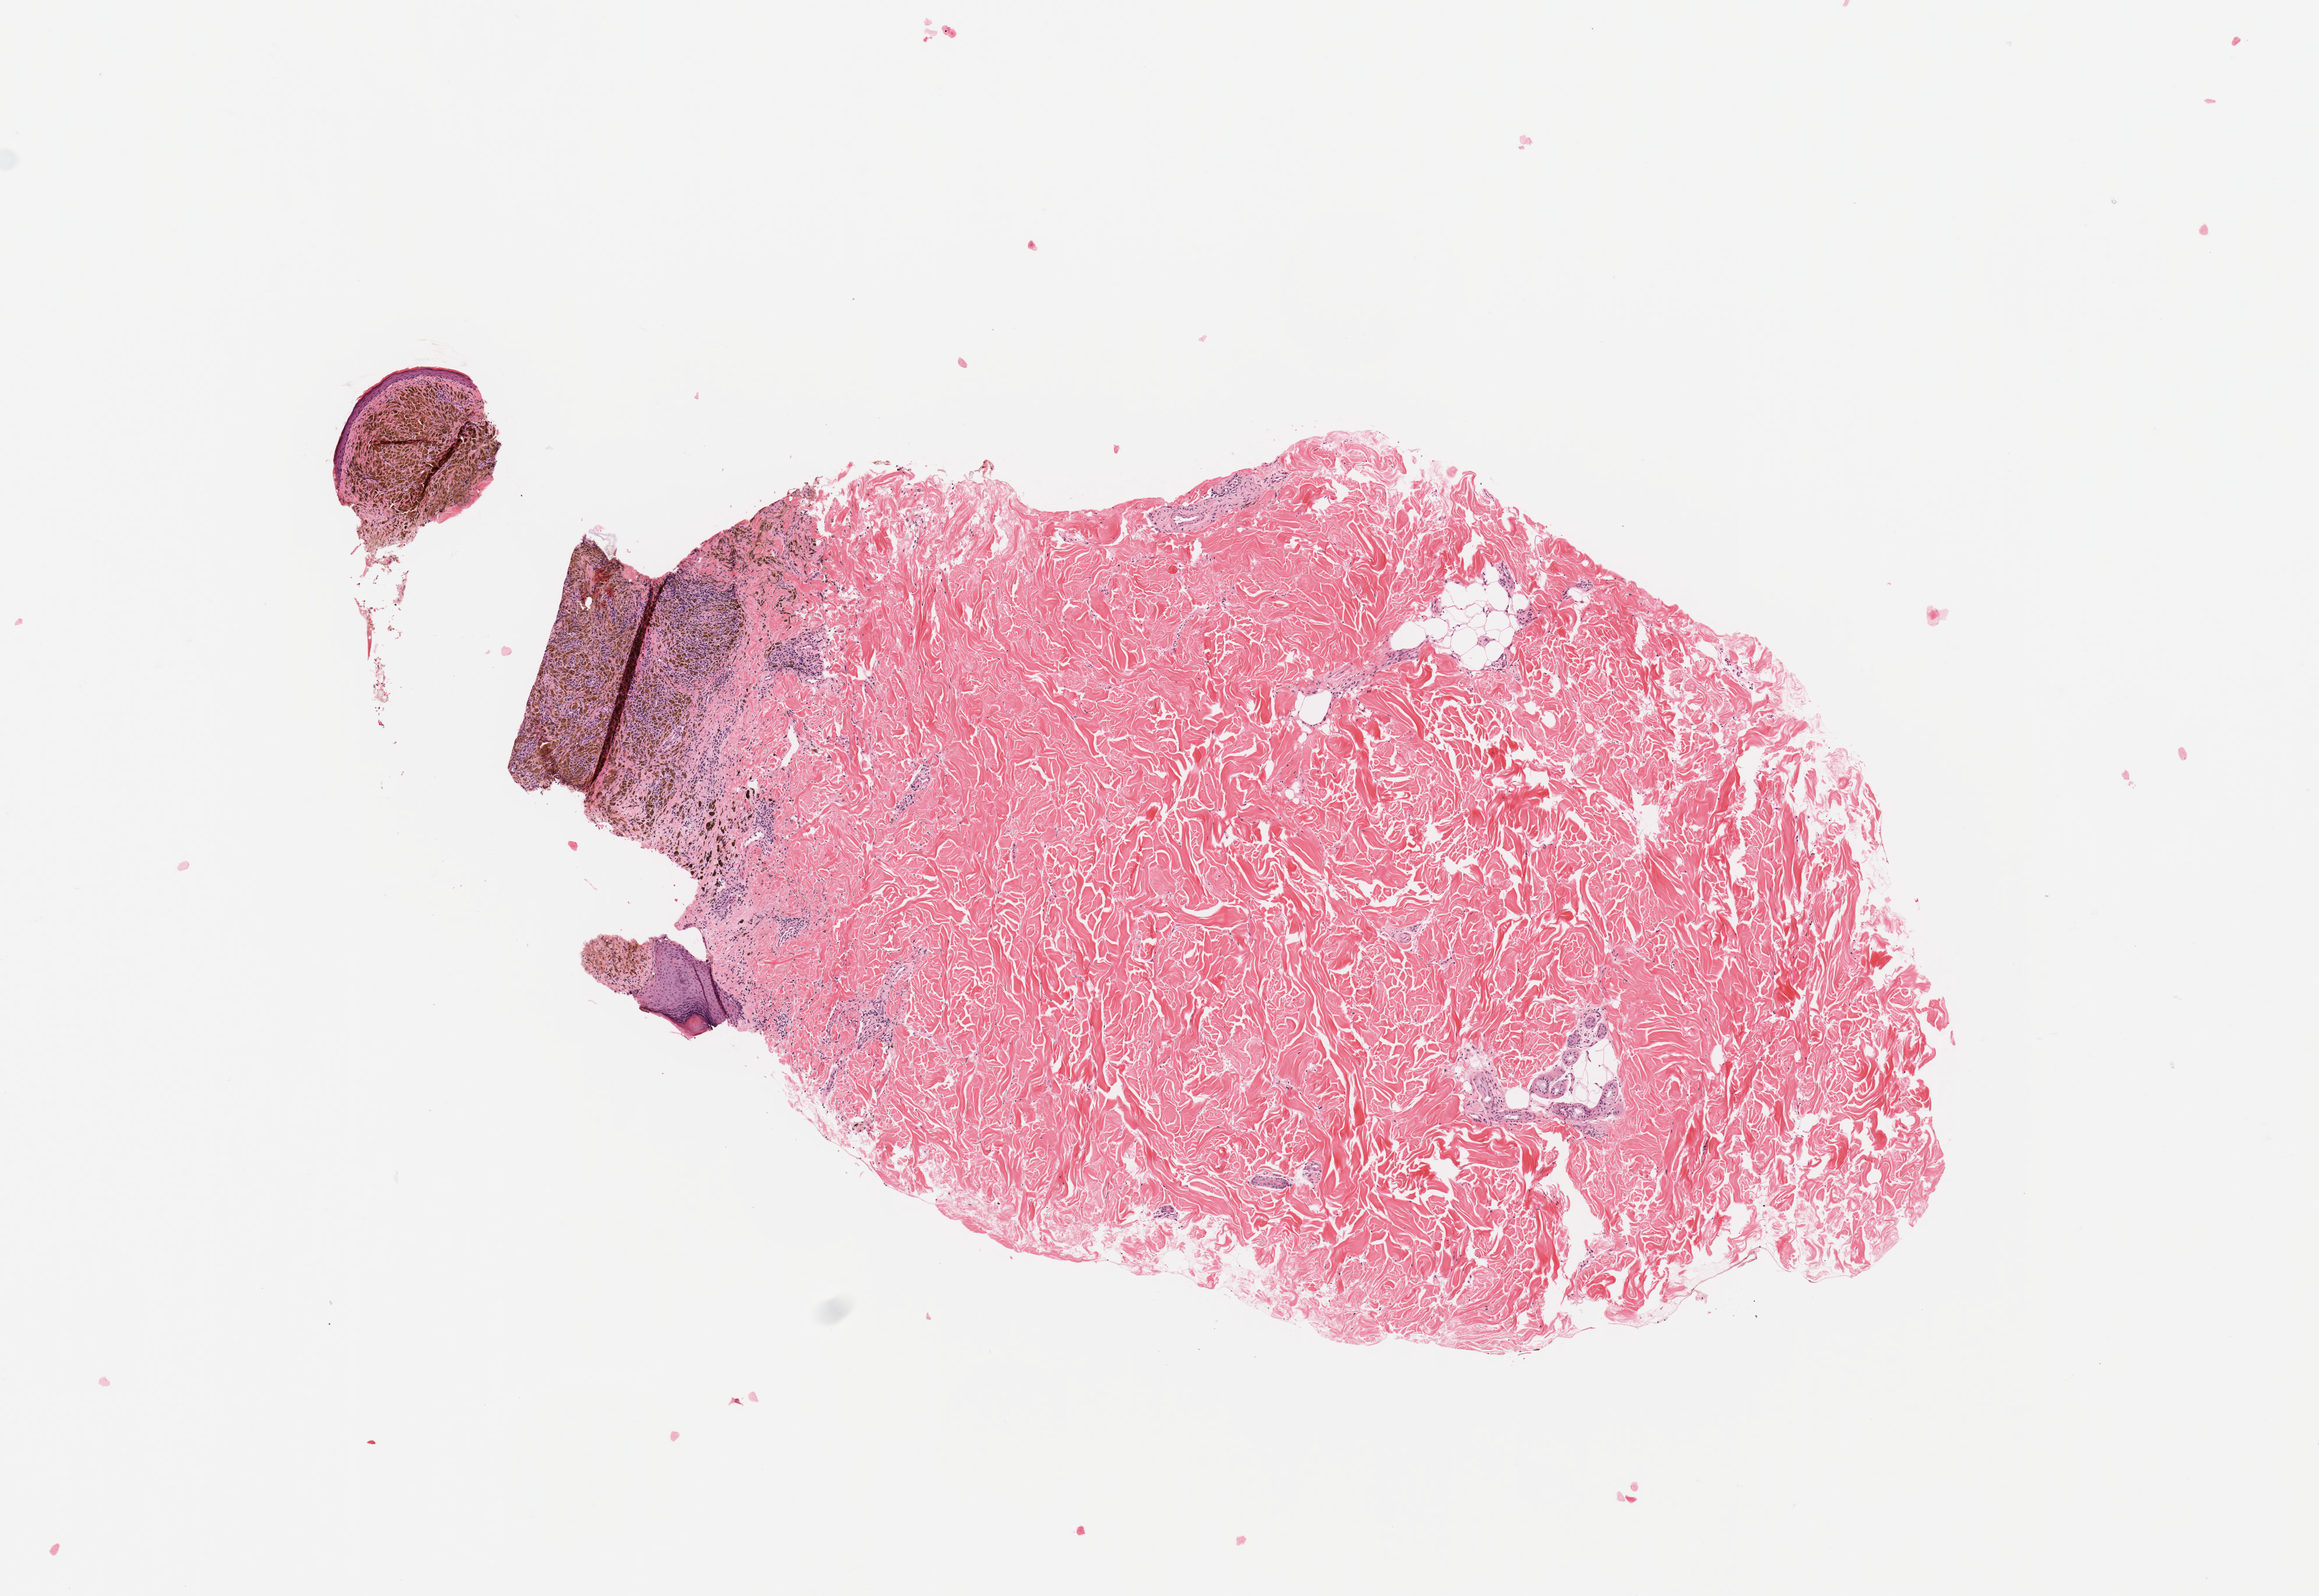
H&E-stained whole-slide image — whole scanned area (about 7.9 x 5.4 mm, slide scanned at 20x) shown as a low-resolution overview; melanoma tumour tissue; sampled site not recorded. Female, 66 y/o.
Primary tumour site (as recorded): head & neck. Patient diagnosis (cohort enrolment): cutaneous melanoma (skin).